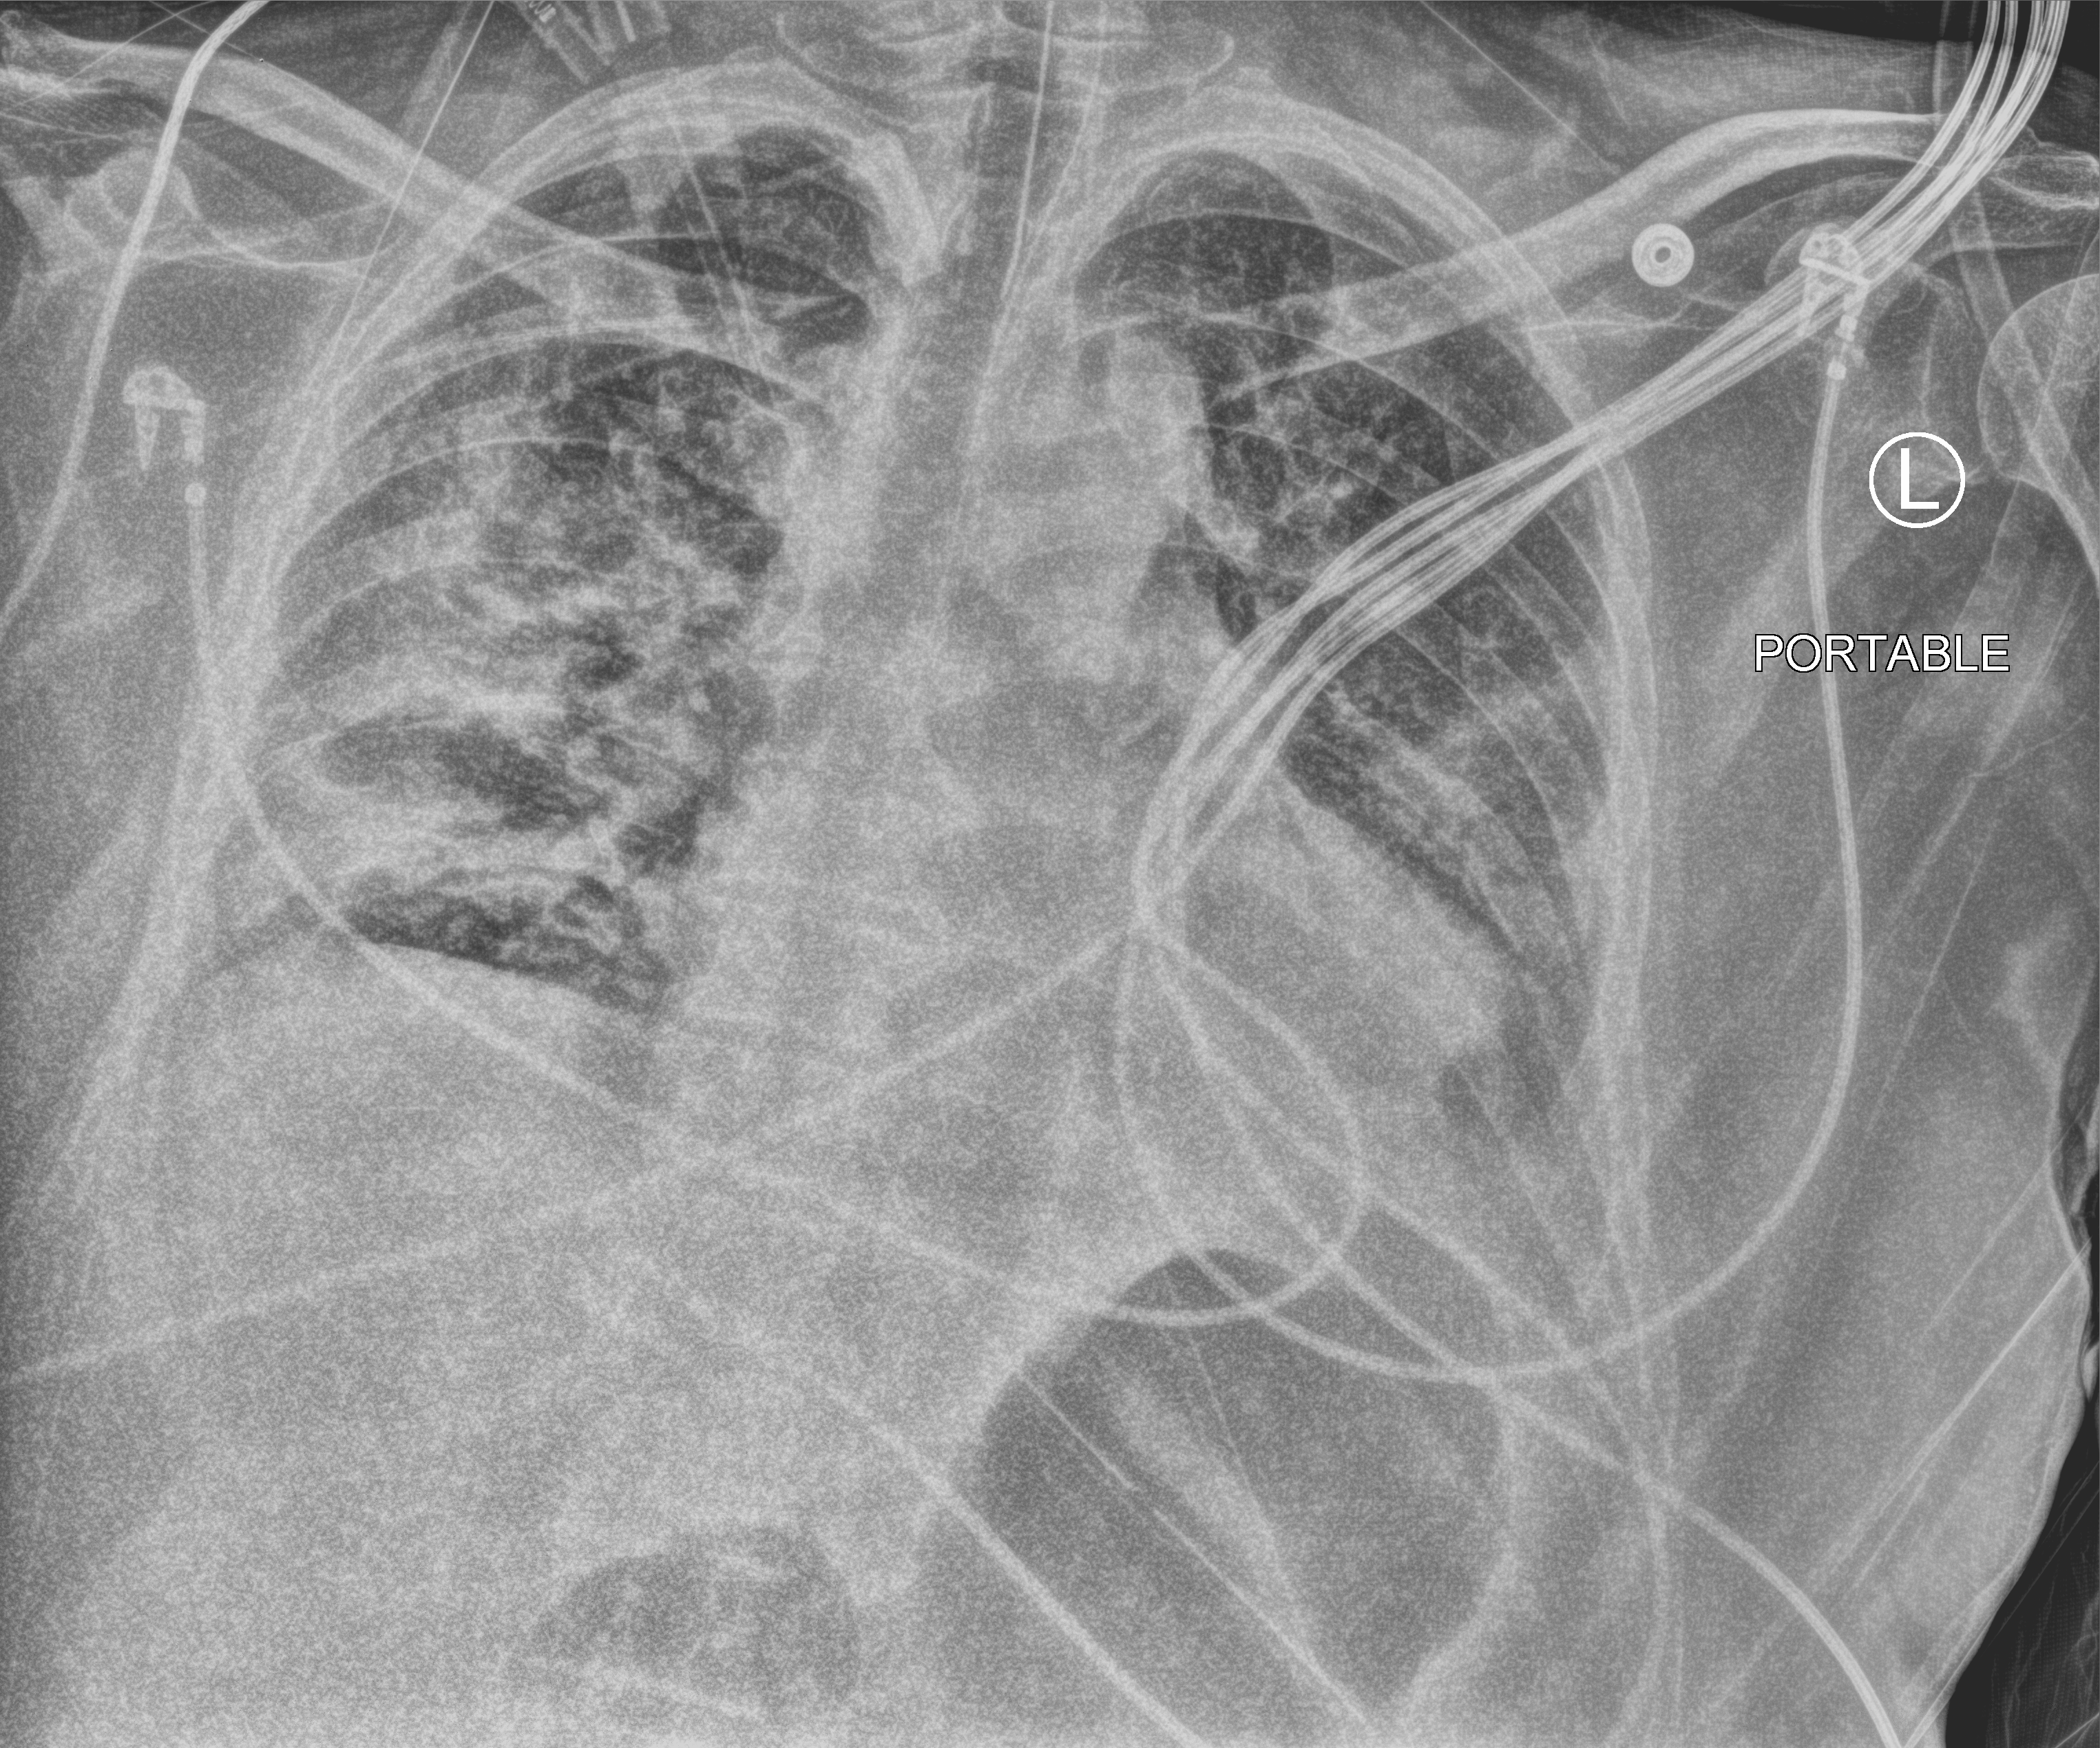
Chest X-ray (portable), anteroposterior (AP) projection. Patient hospitalised with COVID-19; male, aged 60–74 years.
From the hospital-stay record, not from the radiograph (when in the stay this image was taken is not recorded): mechanically ventilated during this hospital stay: yes; COPD (admission record): no.